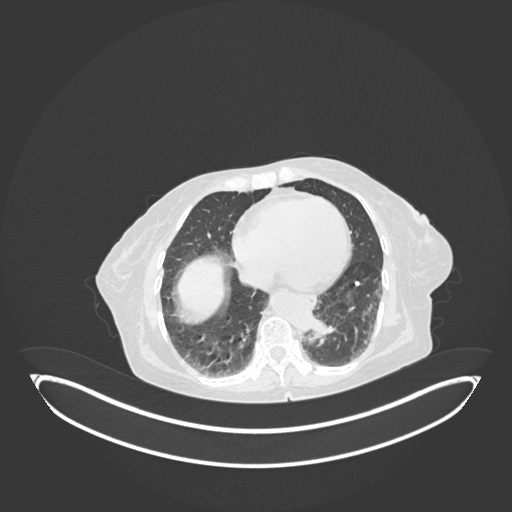
Chest CT, one axial slice. Slice 22 of 189 in the series (ordered by position). 120 kVp. Lung window (W 1500 / L -600 HU). 512 × 512 image matrix, field of view 500 × 500 mm. Patient: female, 82 years. Case-level facts recorded for this patient, not image findings: clinical TNM (as recorded): T1b N0 M1.
Outlined on this slice (rectangle marked by the reading radiologist):
- lung tumour (recorded histology: adenocarcinoma): bounding box (x1, y1, x2, y2) in pixels: (305, 317, 336, 343)